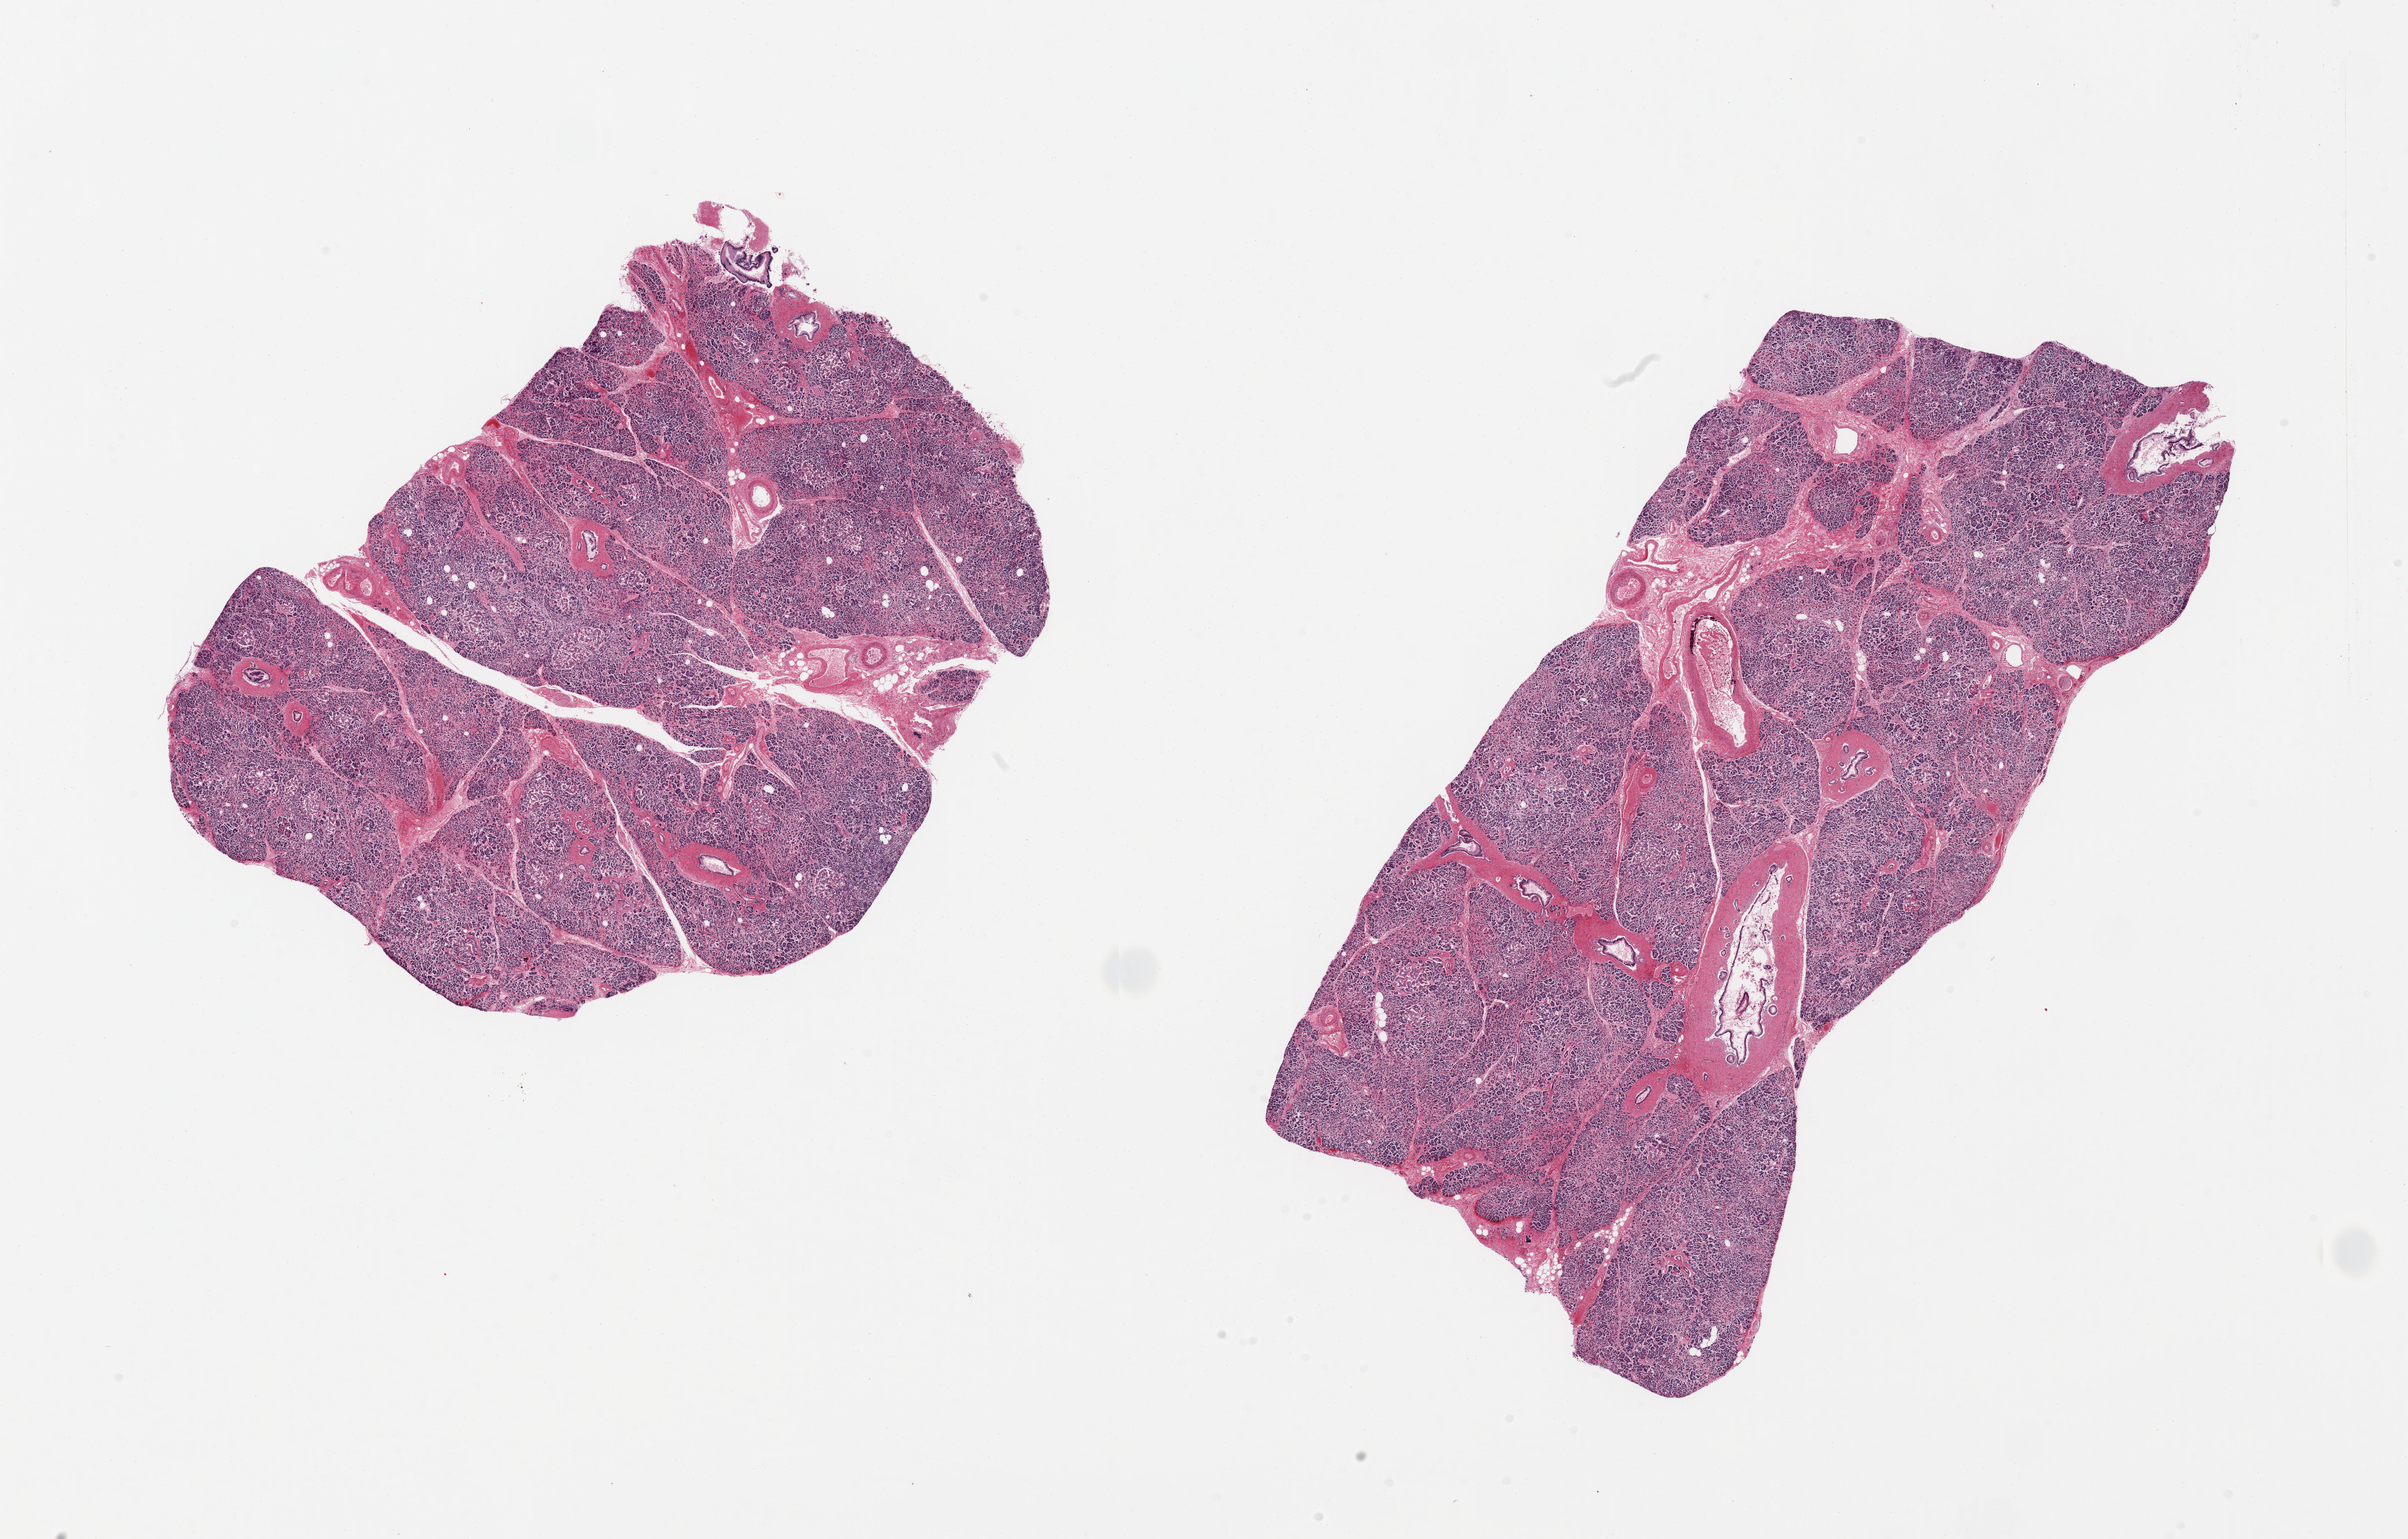
Digitized hematoxylin and eosin (H&E)-stained section, shown as a low-resolution overview of the whole scanned area (about 27.6 x 17.6 mm, slide scanned at 20x); PAXgene-fixed, paraffin-embedded tissue; target tissue: pancreas; tissue donor sample. Donor: female.
Review note (as recorded): 2 pieces, moderately advanced saponification; islets still visible but degenerating.